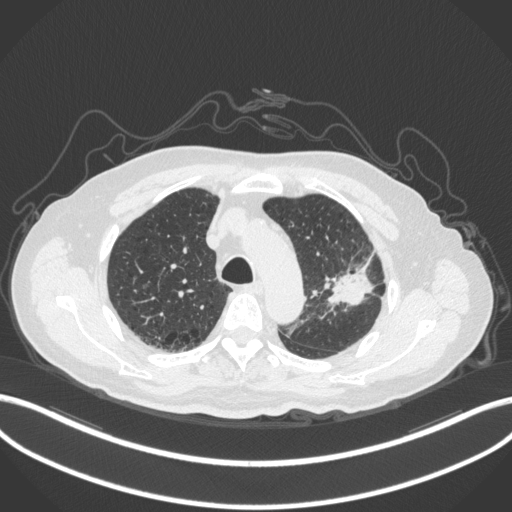
Chest CT, one axial slice; position 224 of 331 along the scan axis; reconstruction kernel B31f; lung window (W 1500 / L -600 HU); 1 mm slice thickness; 512 × 512 image matrix, field of view 400 × 400 mm. Male patient, age 79 years. From the clinical record (not read from this slice): clinical TNM (as recorded): T2a N1 M1; histopathological grade: G3.
Structures marked on this image (rectangle marked by the reading radiologist):
- lung tumour (recorded histology: adenocarcinoma): bounding box (x1, y1, x2, y2) in pixels: (329, 246, 381, 311)